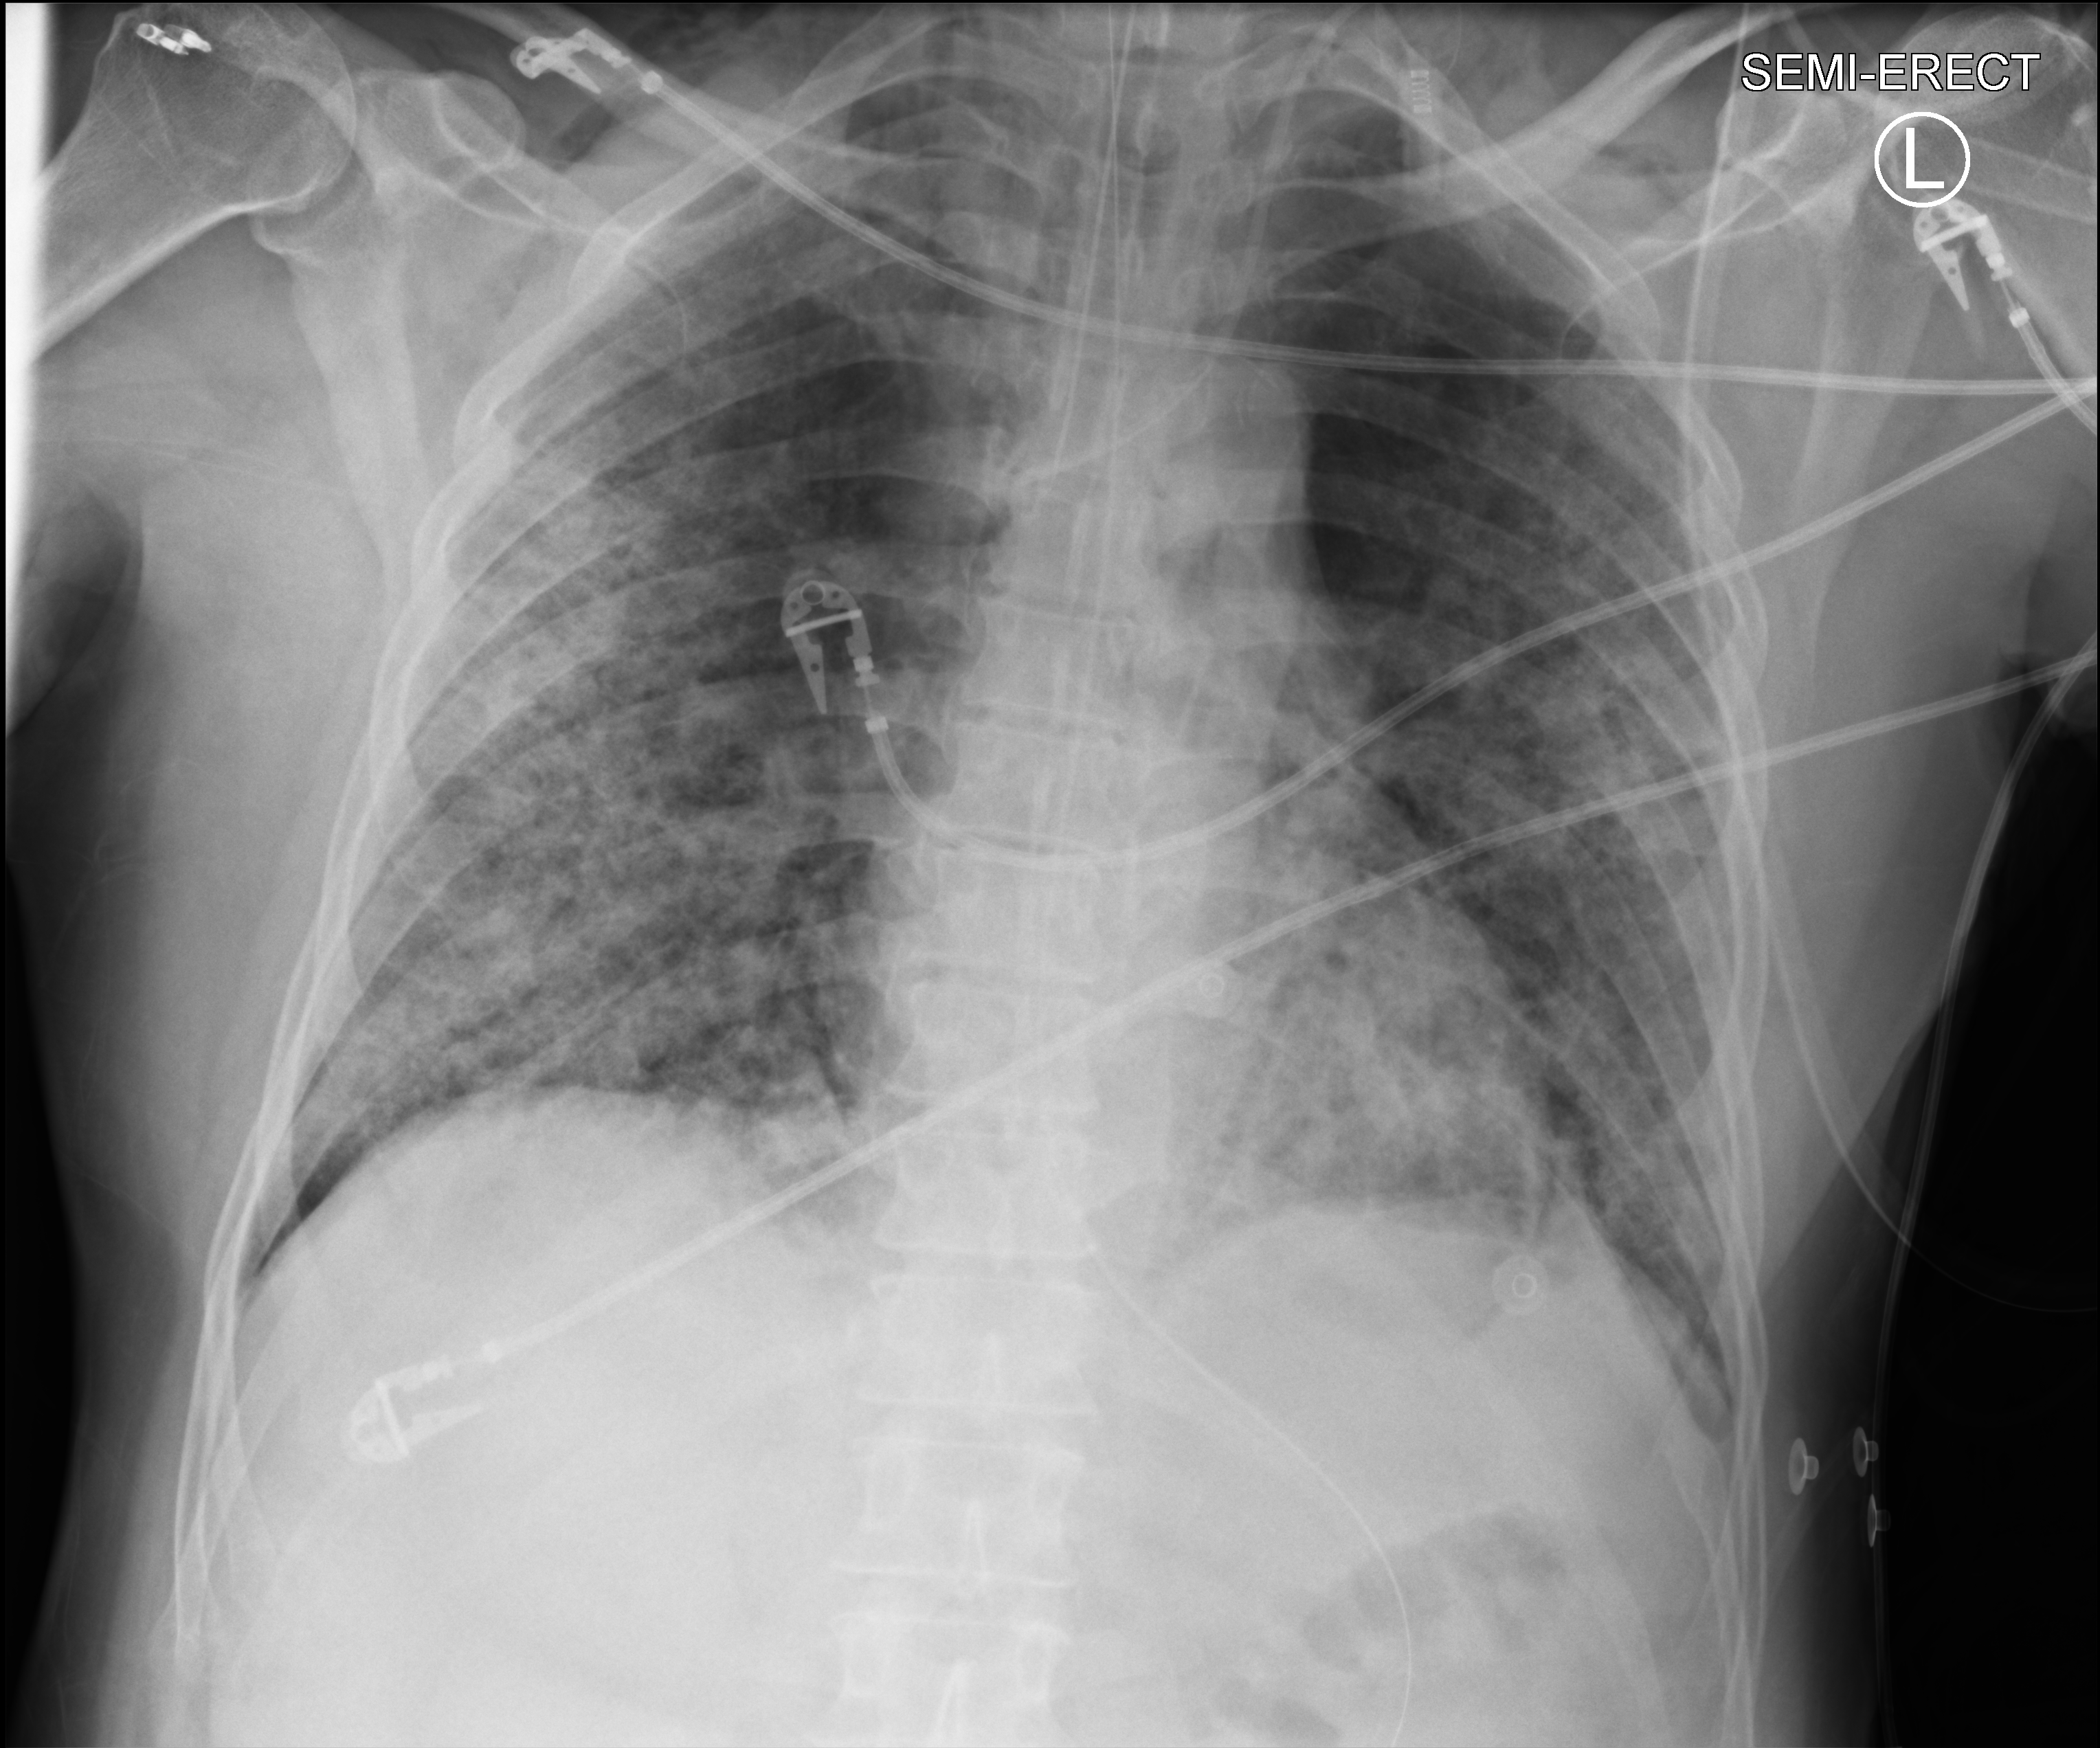
Chest X-ray (portable); anteroposterior (AP) projection. Male patient hospitalised with COVID-19, age 60–74 years.
Admission-level facts for this patient (not findings on this image; timing relative to this image not recorded): COPD (admission record): no; mechanically ventilated during this hospital stay: yes.